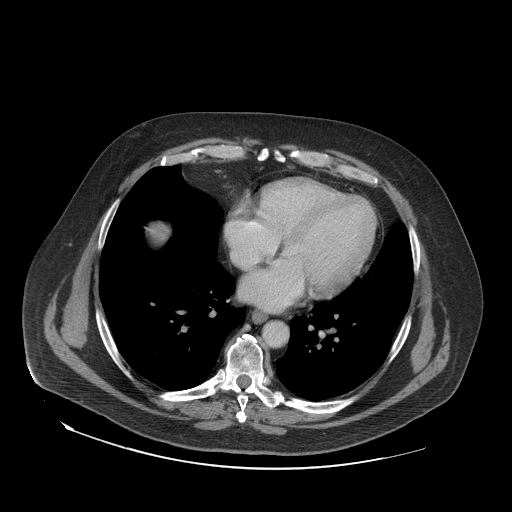
Contrast-enhanced abdominal CT (liver protocol), one axial slice; slice 77 of 79 in the series (ordered by position); reconstruction kernel STANDARD; 140 kVp; soft-tissue window (W 400 / L 40 HU); 2.5 mm slice thickness; 512 × 512 image matrix, field of view 480 × 480 mm. Case-level facts recorded for this patient, not image findings: diagnosis: hepatocellular carcinoma (patient treated with transarterial chemoembolisation; whether this scan precedes or follows treatment is not stated here); TNM stage (as recorded): Stage-IVA; Child-Pugh class: A; tumour differentiation: well differentiated.
Outlined on this slice (semi-automatic segmentation, software-assisted and operator-edited):
- liver parenchyma outside the tumour (the mass and vessels are separate outlines, so this box may not span the whole liver): bounding box <150,224,168,240> (left, top, right, bottom; pixels)